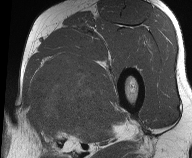
MRI of an extremity soft-tissue mass, one axial slice; slice 38 of 61 in the series (ordered by position); MR volume resampled by the dataset authors to the PET/CT grid (not the native acquisition matrix); 3.27 mm slice thickness; 192 × 158 image matrix, field of view 187 × 154 mm. Male patient. Case-level facts recorded for this patient, not image findings: histological type: pleiomorphic liposarcoma; grade: high; site of the primary tumour: left thigh.
Structures marked on this image (expert contour drawn on MRI and transferred to this co-registered scan by the dataset authors):
- gross tumour volume including surrounding oedema: bounding box [x1, y1, x2, y2] px = [29, 50, 108, 141]
- gross tumour volume (mass): [29, 55, 106, 129]